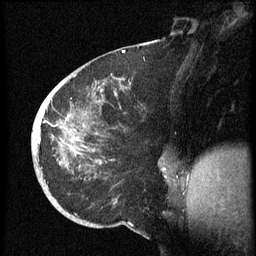
Breast MRI (dynamic contrast-enhanced), one sagittal slice. Slice 27 of 60 in the series (ordered by position). Dynamic contrast-enhanced series, image 2 of 3 at this slice position (ordered by acquisition). 1.5 T. TE 4.2 ms, TR 8.4 ms. 2.5 mm slice thickness. 256 × 256 image matrix. Patient: female, 38 years. From the clinical record (not read from this slice): setting: breast cancer imaged before/during neoadjuvant chemotherapy; receptor status: HER2-positive.
Outlined on this slice (semi-automatic segmentation, software-assisted and operator-edited):
- analysis volume of interest (the breast-tissue region the enhancement analysis was run in; not a lesion): bounding box [x1, y1, x2, y2] px = [32, 74, 173, 202]
- tumour enhancement mask (voxels above the 70 % enhancement threshold inside the analysis volume of interest): [36, 79, 167, 172]